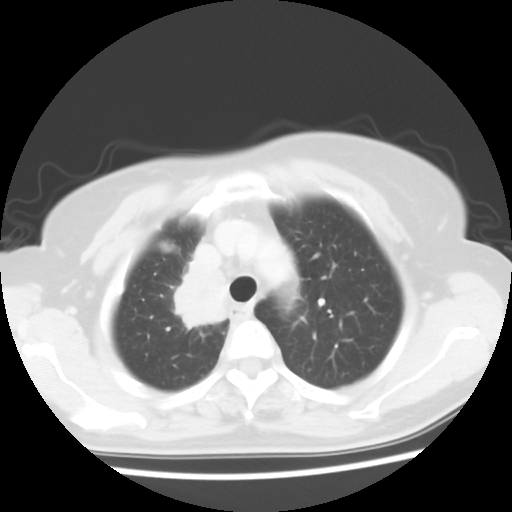
Chest CT, one axial slice. Position 45 of 56 along the scan axis. 120 kVp. Lung window (W 1500 / L -600 HU). 5 mm slice thickness. 512 × 512 image matrix, field of view 314 × 314 mm. Patient: female, 62 years. Case-level facts recorded for this patient, not image findings: clinical TNM (as recorded): T2 N1 M1a.
Structures marked on this image (rectangle marked by the reading radiologist):
- lung tumour (recorded histology: adenocarcinoma): box from (x=172, y=256) to (x=236, y=336) px